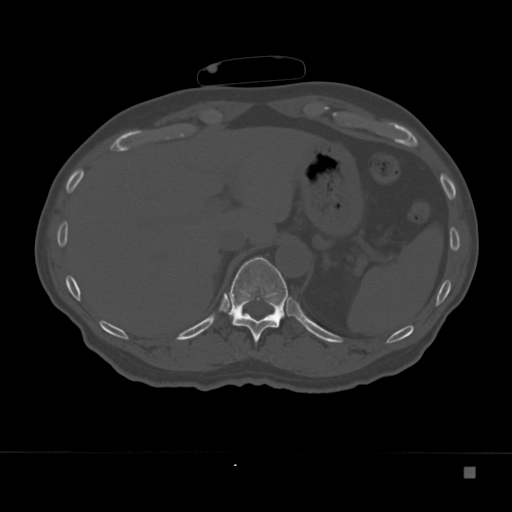
CT including the spine, one axial slice. Position 152 of 332 along the scan axis. Reconstruction kernel Br40s. Bone window (W 1800 / L 400 HU). 1.5 mm slice thickness. 512 × 512 image matrix. Patient: male, 72 years. From the clinical record (not read from this slice): primary cancer: skeletal.
Outlined on this slice (semi-automatic segmentation, software-assisted and operator-edited):
- T11 vertebra: bounding box [x1, y1, x2, y2] px = [229, 257, 288, 344]